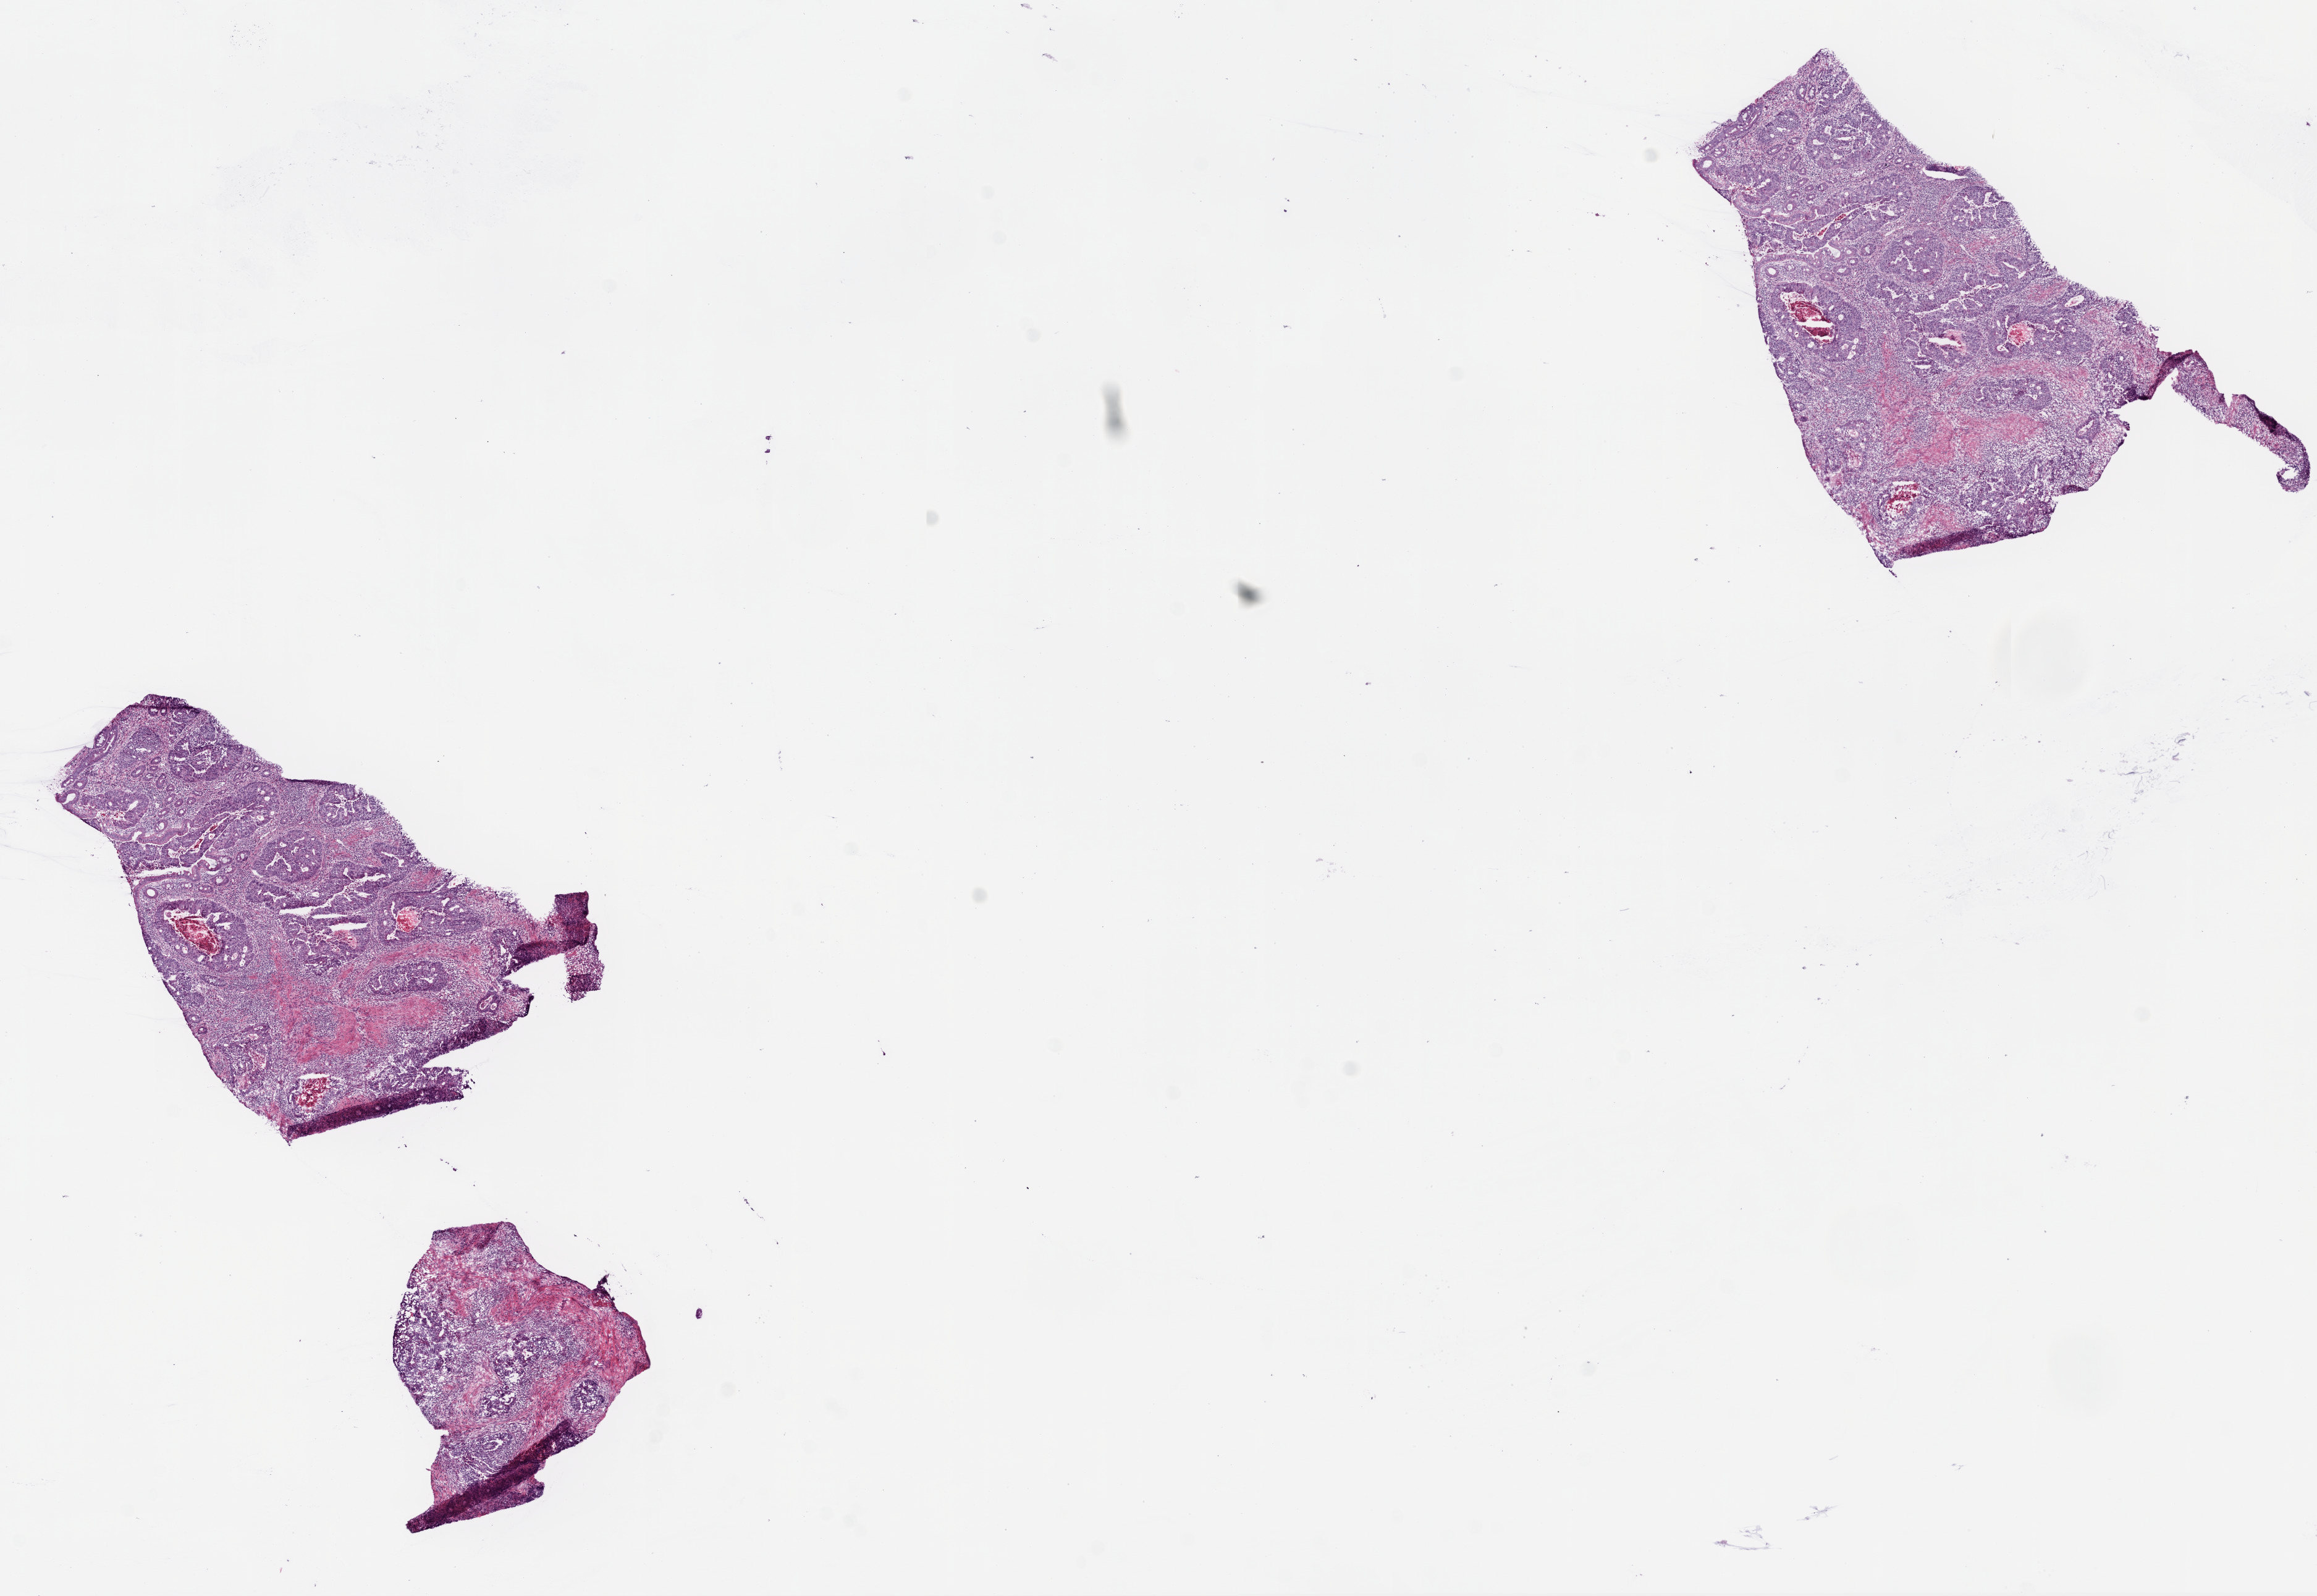
Digitized Hematoxylin and eosin (H&E) stained tissue section (whole slide), a low-resolution overview of the entire scanned area, about 15.0 x 10.4 mm (from a 20x scan). Frozen section from the bottom of the tissue portion. Colon, primary tumour sample. Patient: male, age at initial diagnosis 75 years. Composition of this section per pathologist review: tumour cells 75%, tumour nuclei 65%, normal cells 0%, stromal cells 23%, necrosis 2%. Infiltration values recorded for this section: lymphocyte infiltration 30%, neutrophil infiltration 1%.
Pathologic diagnosis: Adenocarcinoma, NOS. Lymph nodes positive (case pathology): 3 of 13 examined. AJCC pathologic stage: IIIB (6th edition).